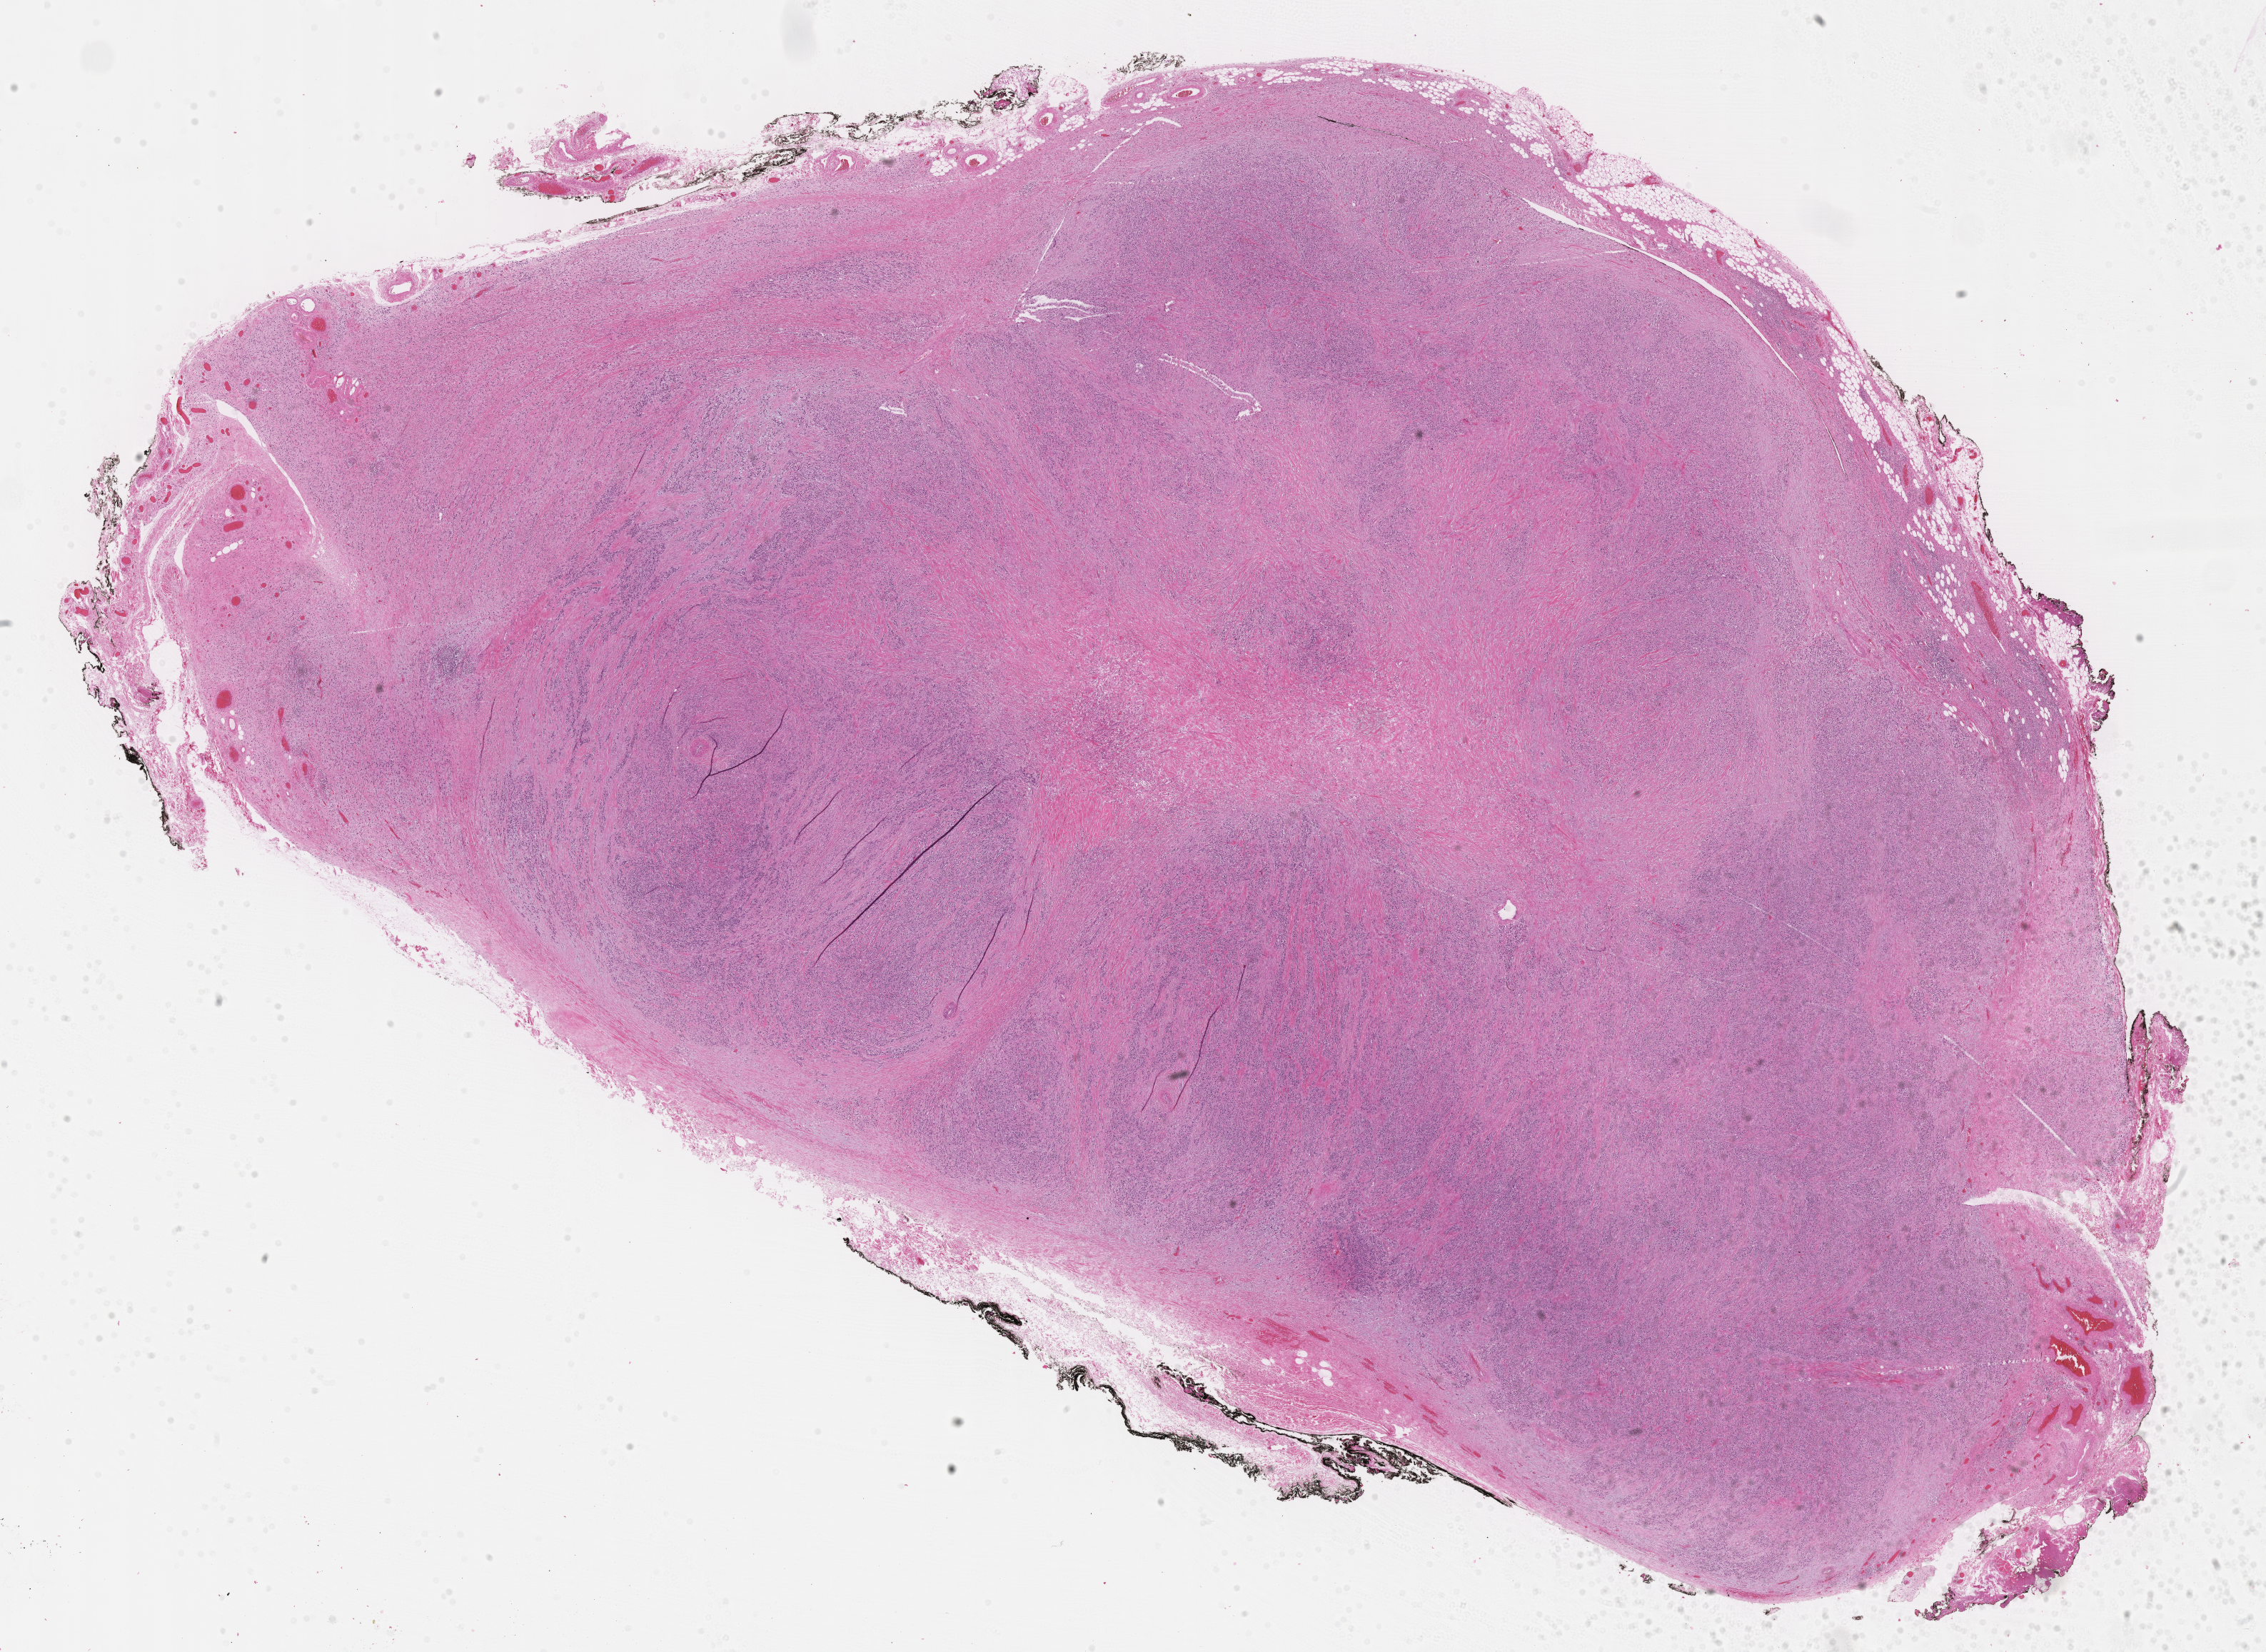
Whole-slide image, H&E stain of tumor tissue, low-resolution overview of the scanned area, about 25.7 x 18.7 mm; formalin-fixed, paraffin-embedded (FFPE) tissue; sample anatomic site: testicle-right (extratesticular). Male patient, age at diagnosis 20.3 years.
• diagnosis: rhabdomyosarcoma; histological classification: embryonal rhabdomyosarcoma
• stage (as recorded): 1
• metastatic status at presentation (as recorded): non-metastatic
• primary site (case record): testis-Paratestis